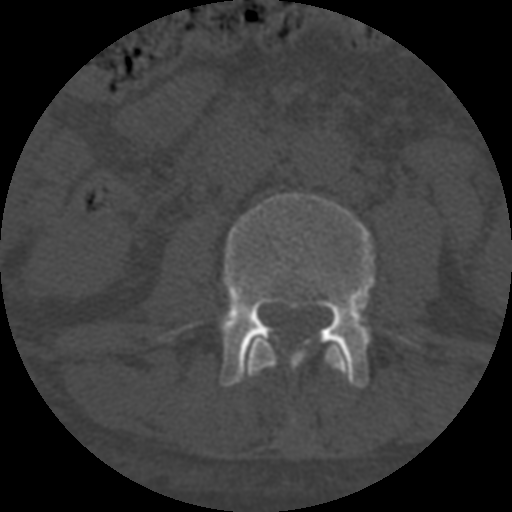
CT including the spine, one axial slice. Position 241 of 708 along the scan axis. Reconstruction kernel STANDARD. 120 kVp. One of 3 acquisitions stored at this slice position. Bone window (W 1800 / L 400 HU). 1.25 mm slice thickness. 512 × 512 image matrix. Patient age 55 years. From the clinical record (not read from this slice): primary cancer: colon; vertebrae with lytic lesions (as recorded): T12, L1, L5.
Outlined on this slice (semi-automatically segmented with operator editing):
- L2 vertebra: box from (x=246, y=338) to (x=346, y=427) px
- L3 vertebra: (x=154, y=192)–(x=426, y=388)